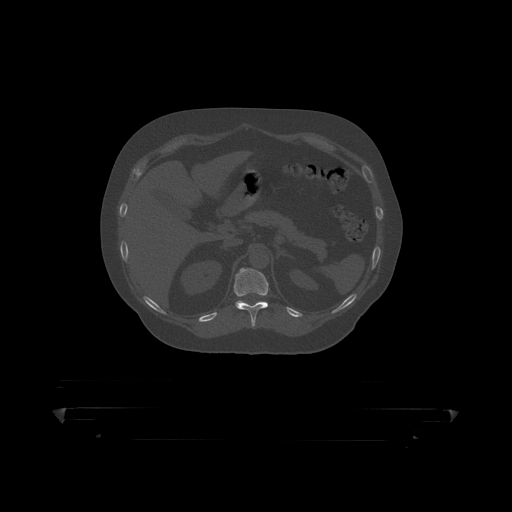
CT including the spine, one axial slice. Slice 191 of 390 in the series (ordered by position). 120 kVp. Bone window (W 1800 / L 400 HU). 1.25 mm slice thickness. 512 × 512 image matrix, field of view 650 × 650 mm. Male patient, age 60 years. From the clinical record (not read from this slice): primary cancer: prostate.
Structures marked on this image (semi-automatic segmentation, software-assisted and operator-edited):
- T11 vertebra: bounding box (x1, y1, x2, y2) in pixels: (234, 268, 291, 319)